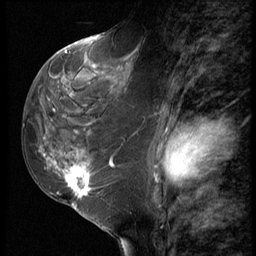
Breast MRI (dynamic contrast-enhanced), one sagittal slice. Slice 31 of 62 in the series (ordered by position). 3 images stored at this slice position (order not interpretable as contrast timing). 1.5 T. TE 4.2 ms, TR 9 ms. 256 × 256 image matrix, field of view 180 × 180 mm. Patient: female, 50 years. Case-level facts recorded for this patient, not image findings: setting: breast cancer imaged before/during neoadjuvant chemotherapy; receptor status: HR-positive, HER2-negative.
Structures marked on this image (semi-automatically segmented with operator editing):
- analysis volume of interest (the breast-tissue region the enhancement analysis was run in; not a lesion): bounding box [x1, y1, x2, y2] px = [32, 91, 118, 209]
- tumour enhancement mask (voxels above the 140 % enhancement threshold inside the analysis volume of interest): [67, 158, 113, 205]